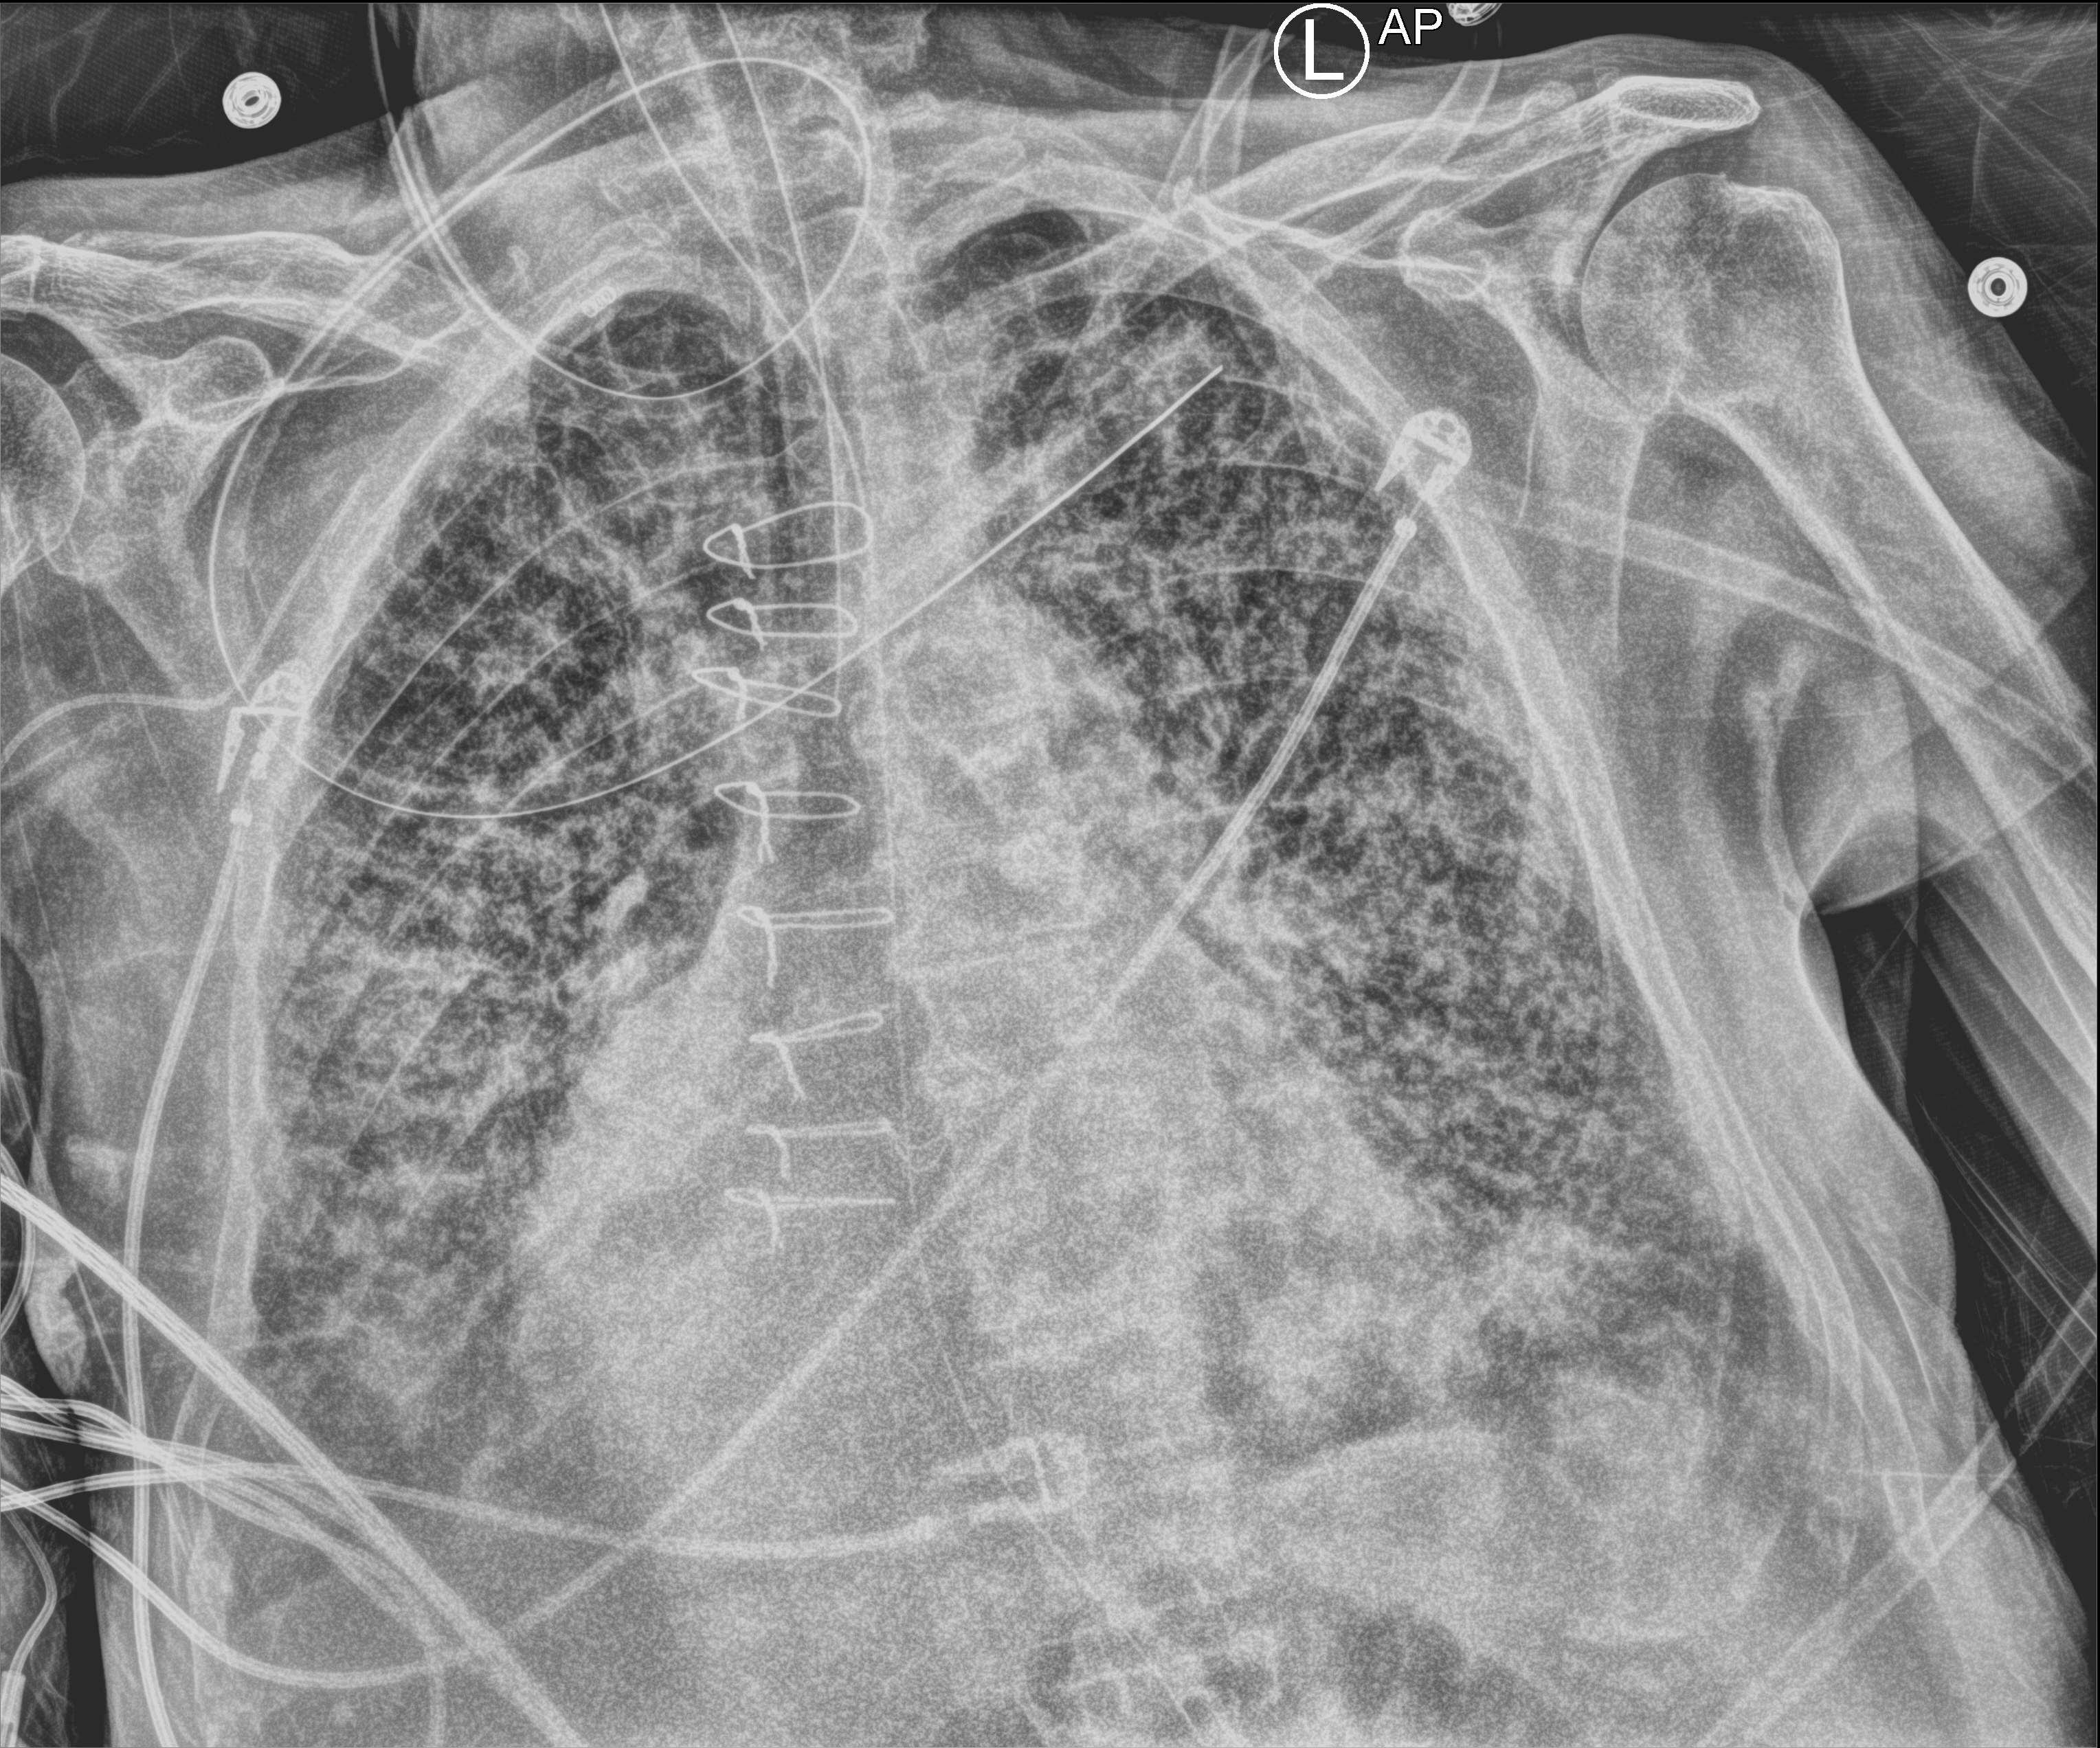
Portable chest radiograph; anteroposterior (AP) projection. Patient hospitalised with COVID-19; male, aged 75–90 years.
Hospital-stay facts (about this admission, not read from this image; timing relative to this image not recorded): mechanically ventilated during this hospital stay: yes.